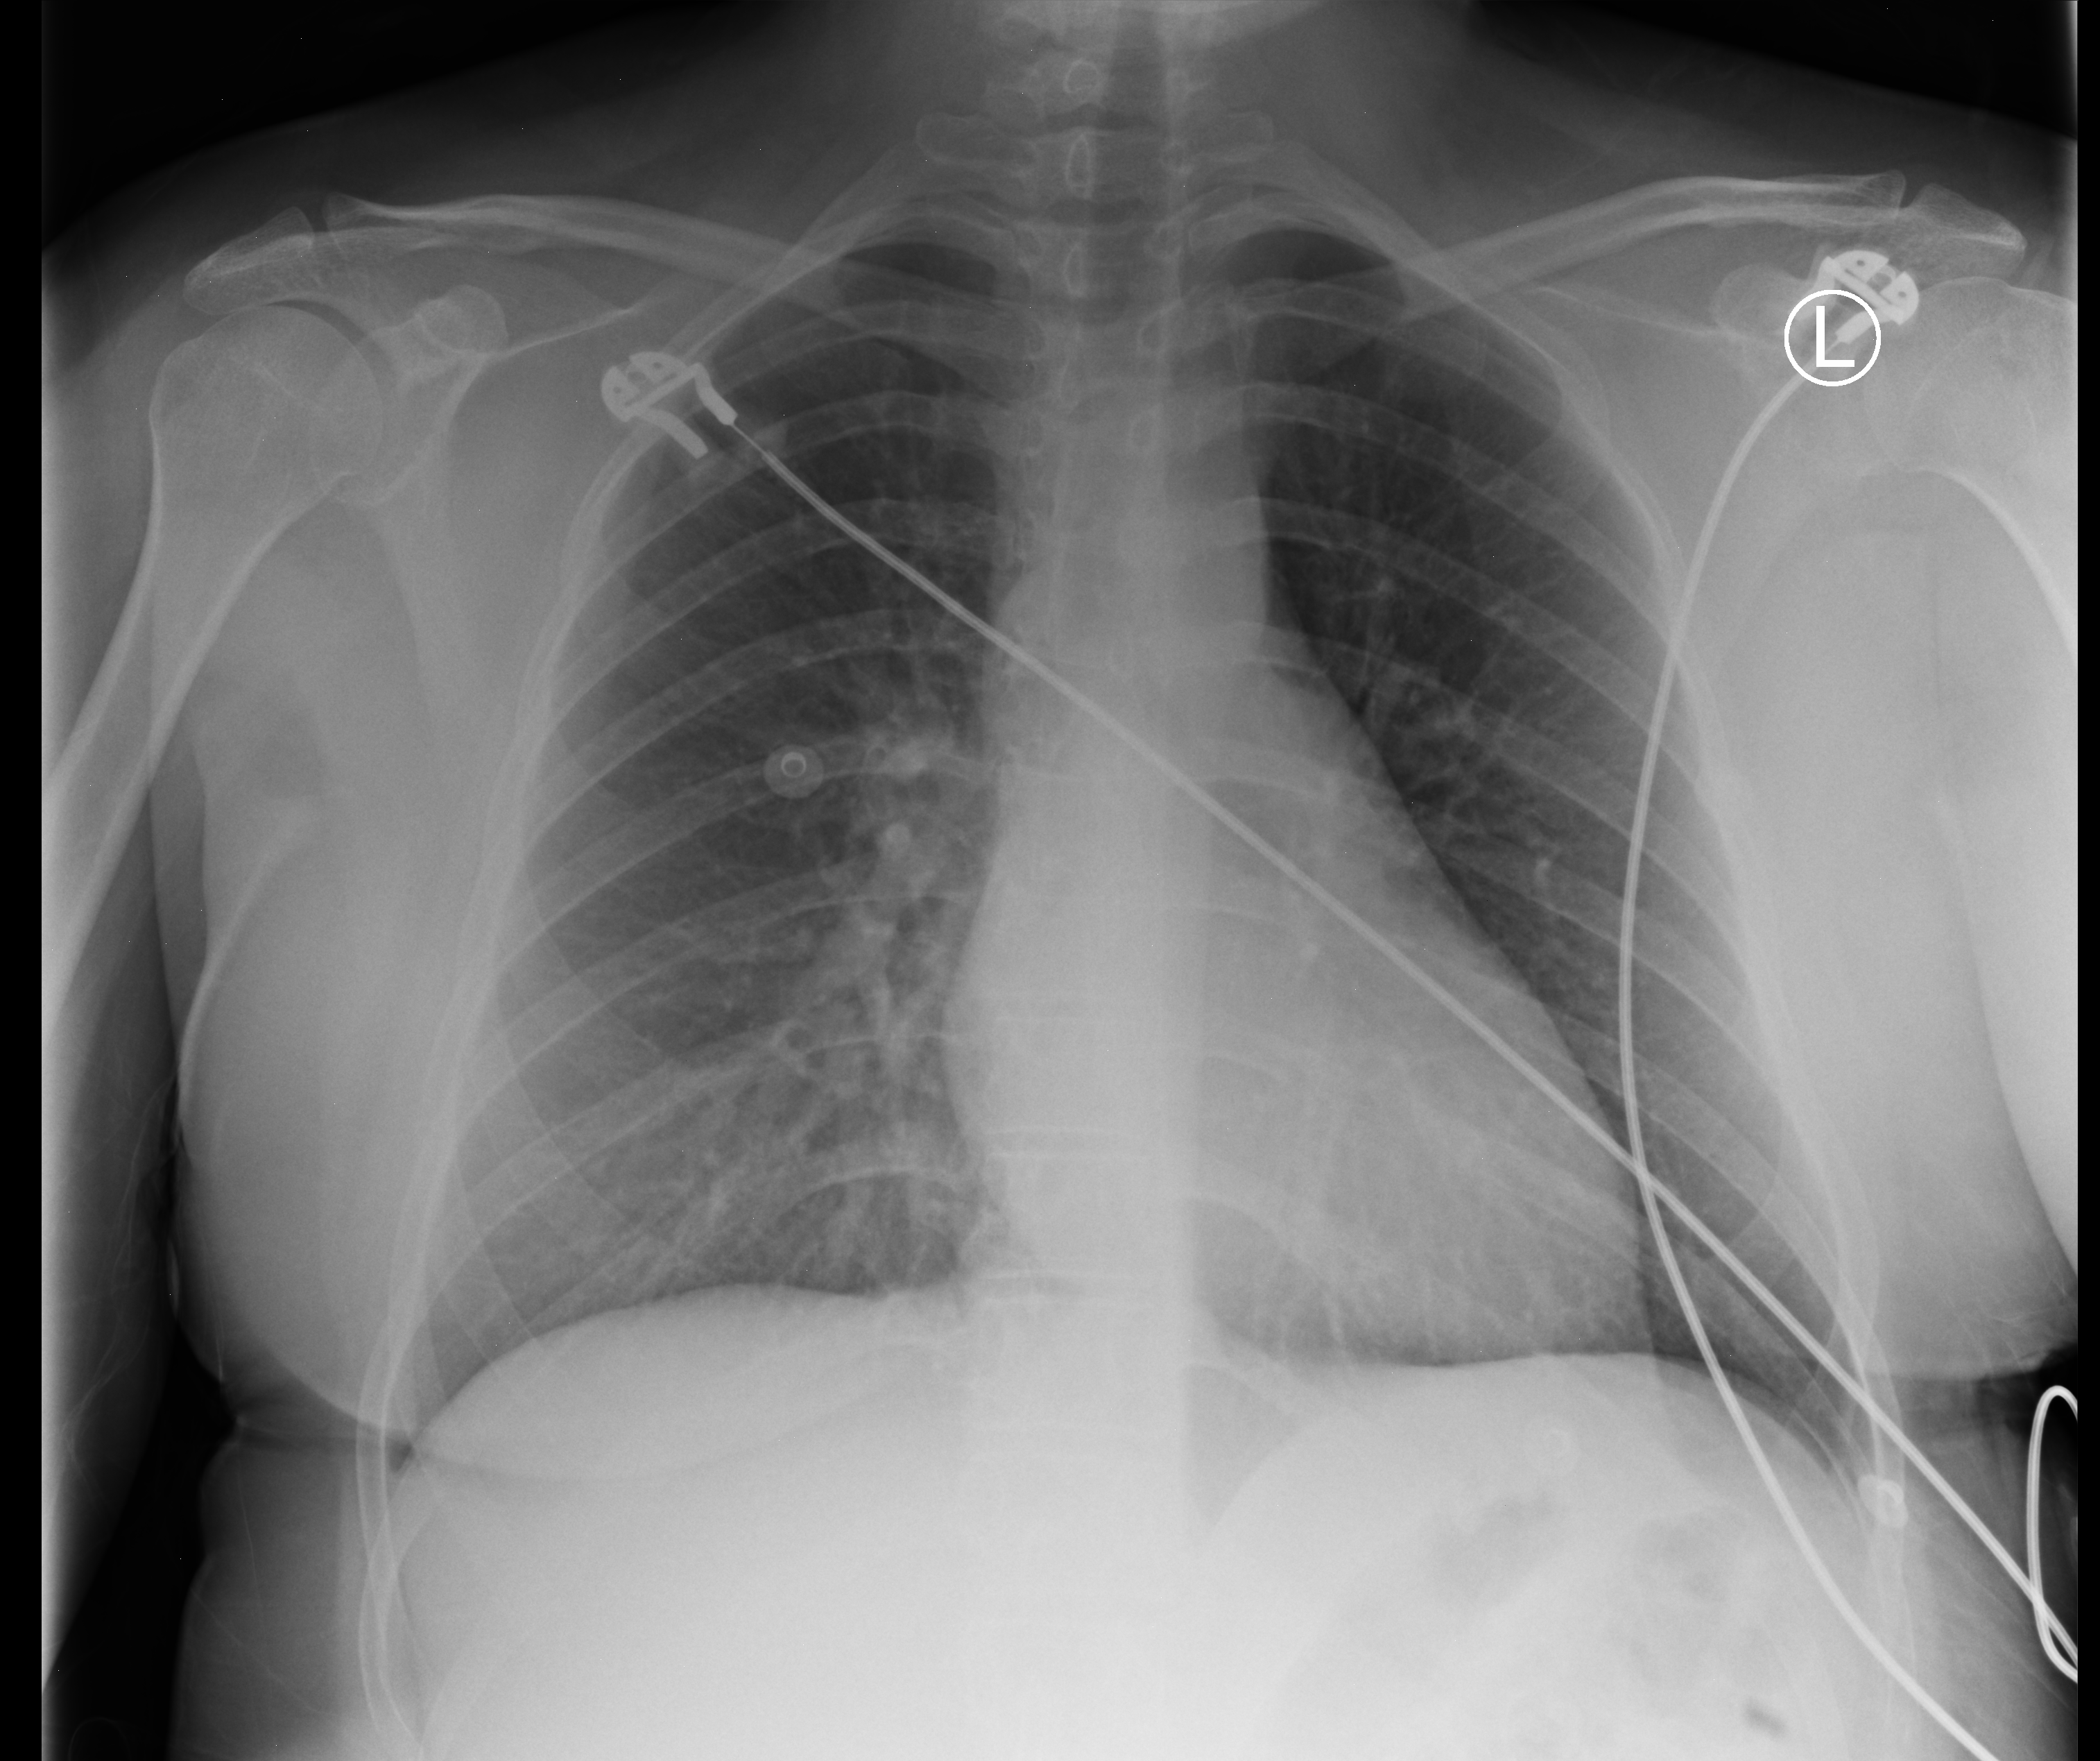
Chest X-ray (portable). Patient hospitalised with COVID-19; female, aged 18–59 years.
From the hospital-stay record, not from the radiograph (when in the stay this image was taken is not recorded): length of hospital stay: 1 day.